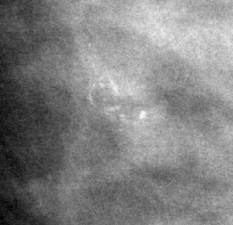
Cropped region of a digitized screen-film mammogram centred on a radiologist-marked abnormality; right breast; CC view; BI-RADS breast density category 2 (scale 1–4).
- Finding: calcifications, morphology pleomorphic, distribution clustered; BI-RADS assessment category 4; pathology result (as recorded, not read from the image): benign.